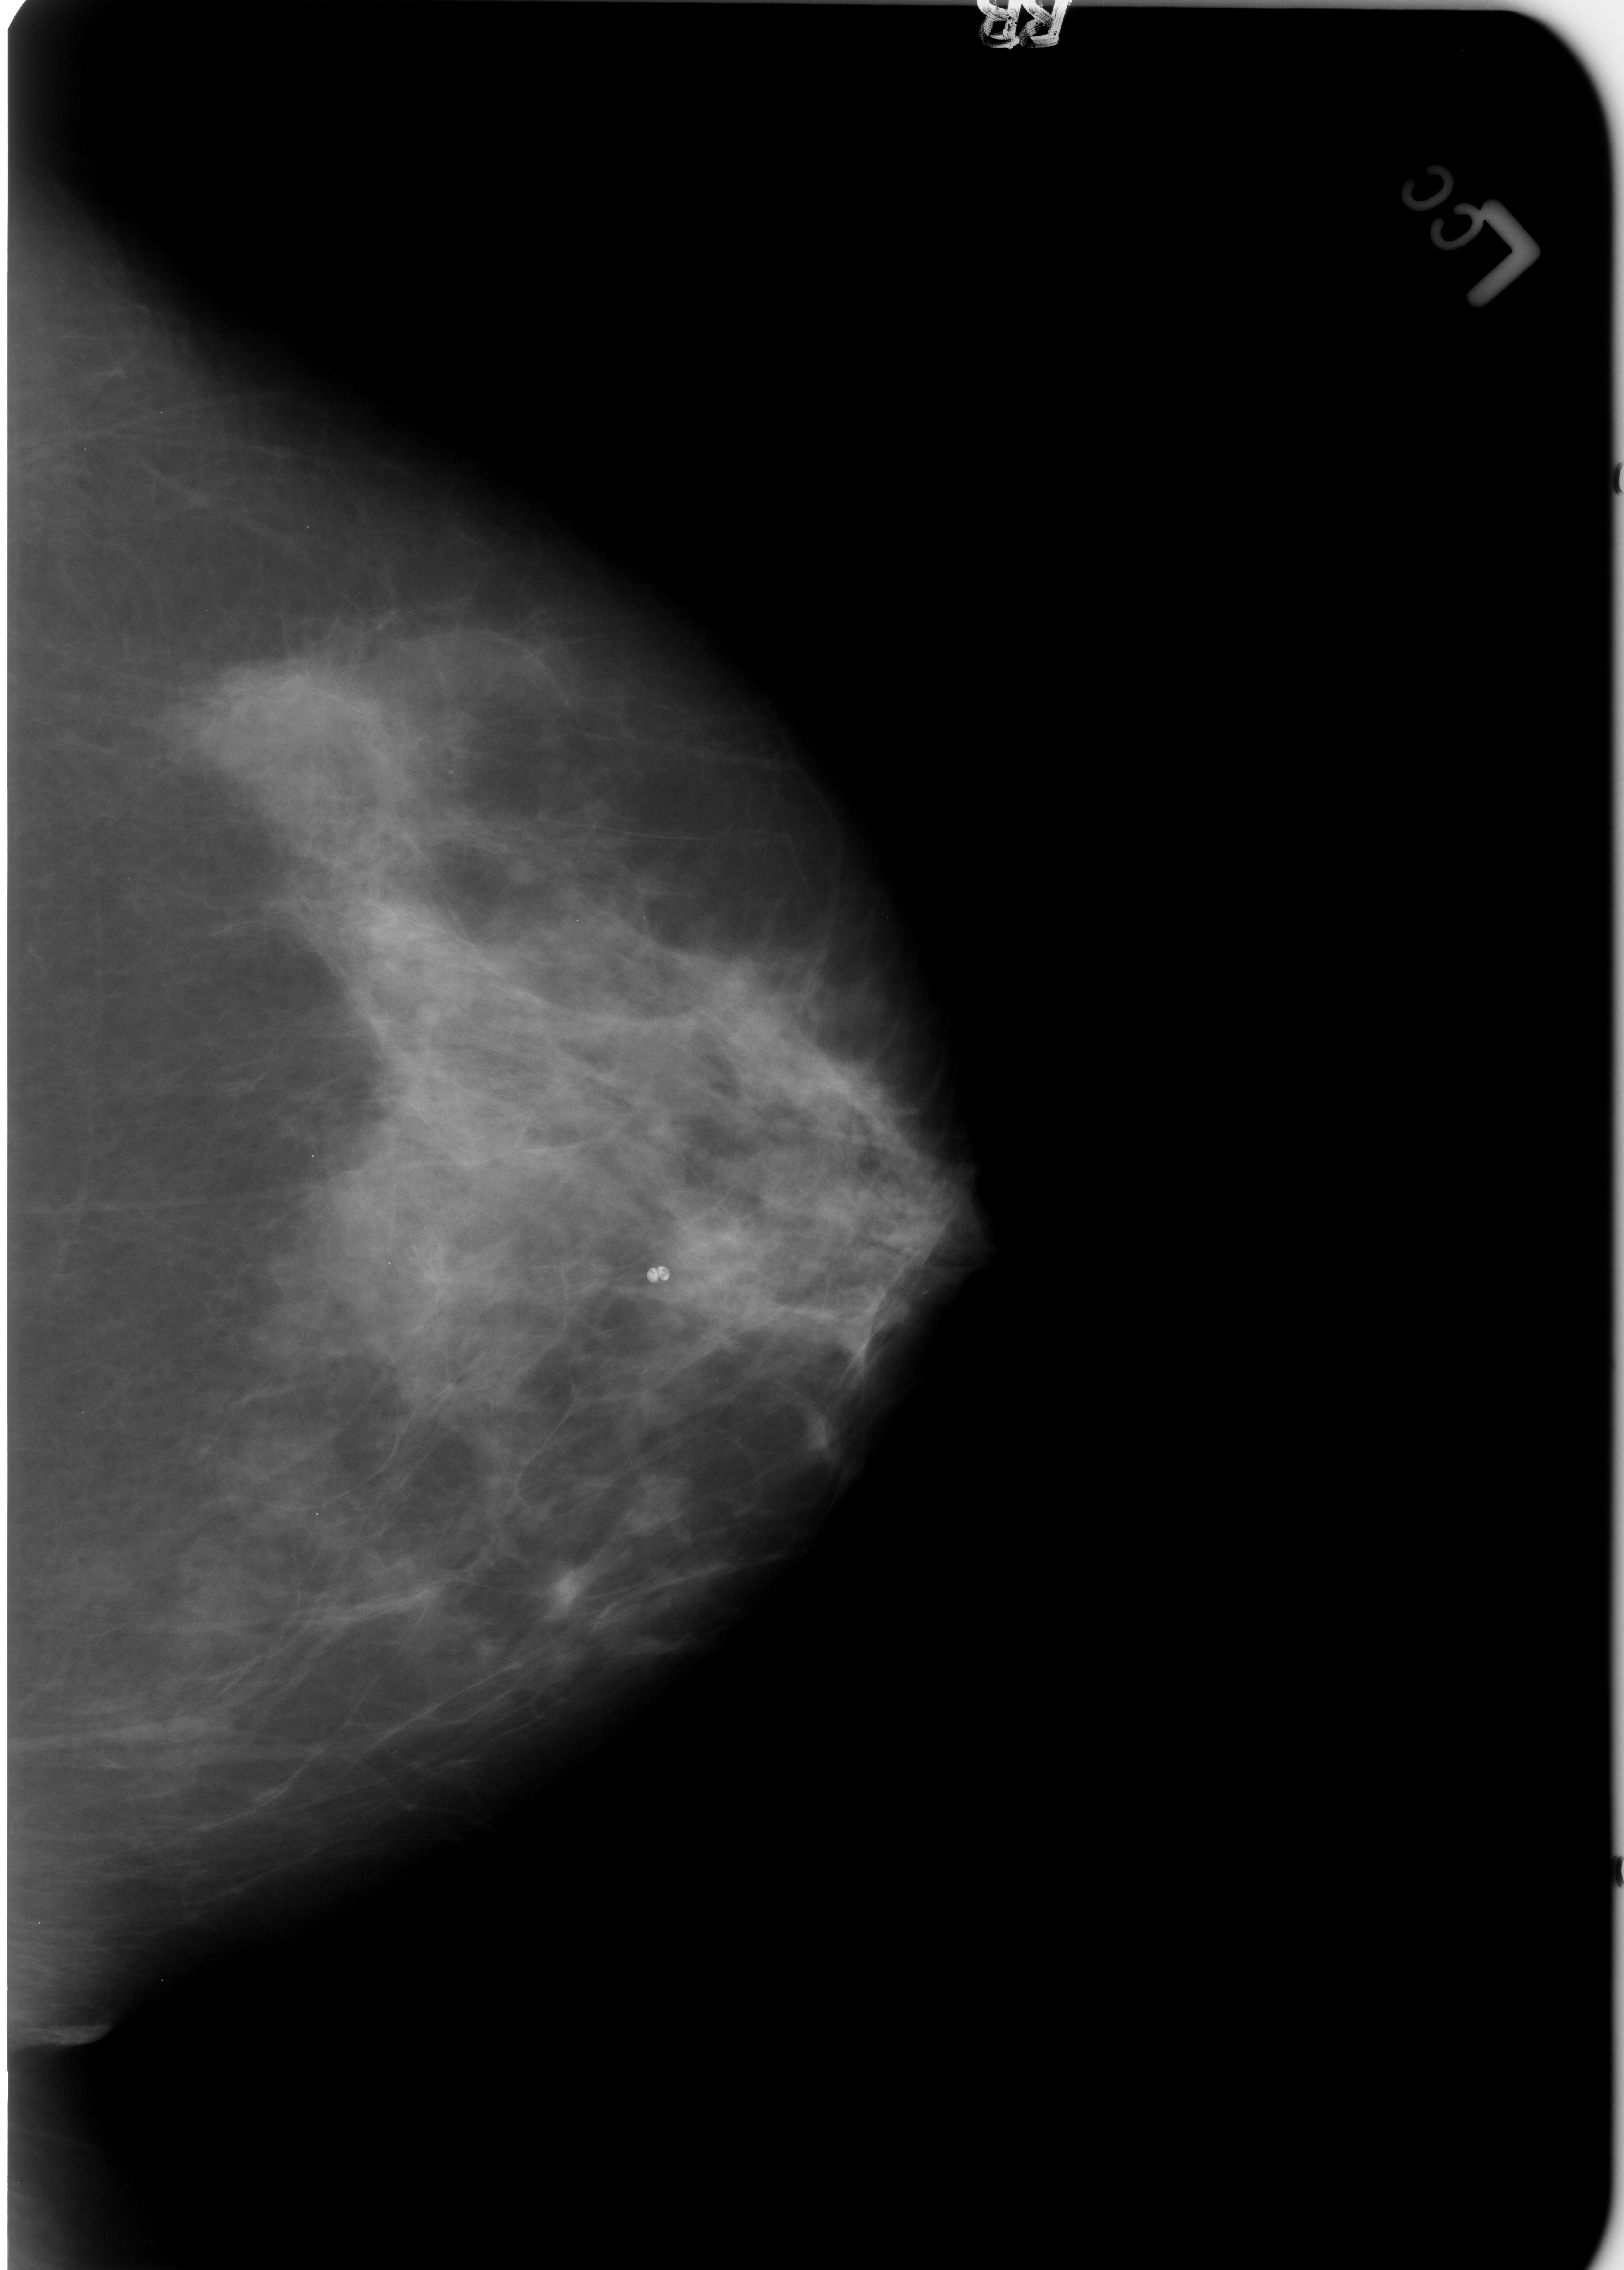
Mammogram (digitized film), left breast, craniocaudal (CC) view, breast composition: heterogeneously dense (BI-RADS density category 3 of 4).
Marked abnormality: calcifications, morphology lucent center; BI-RADS assessment category 2; benign without callback (not worked up further).